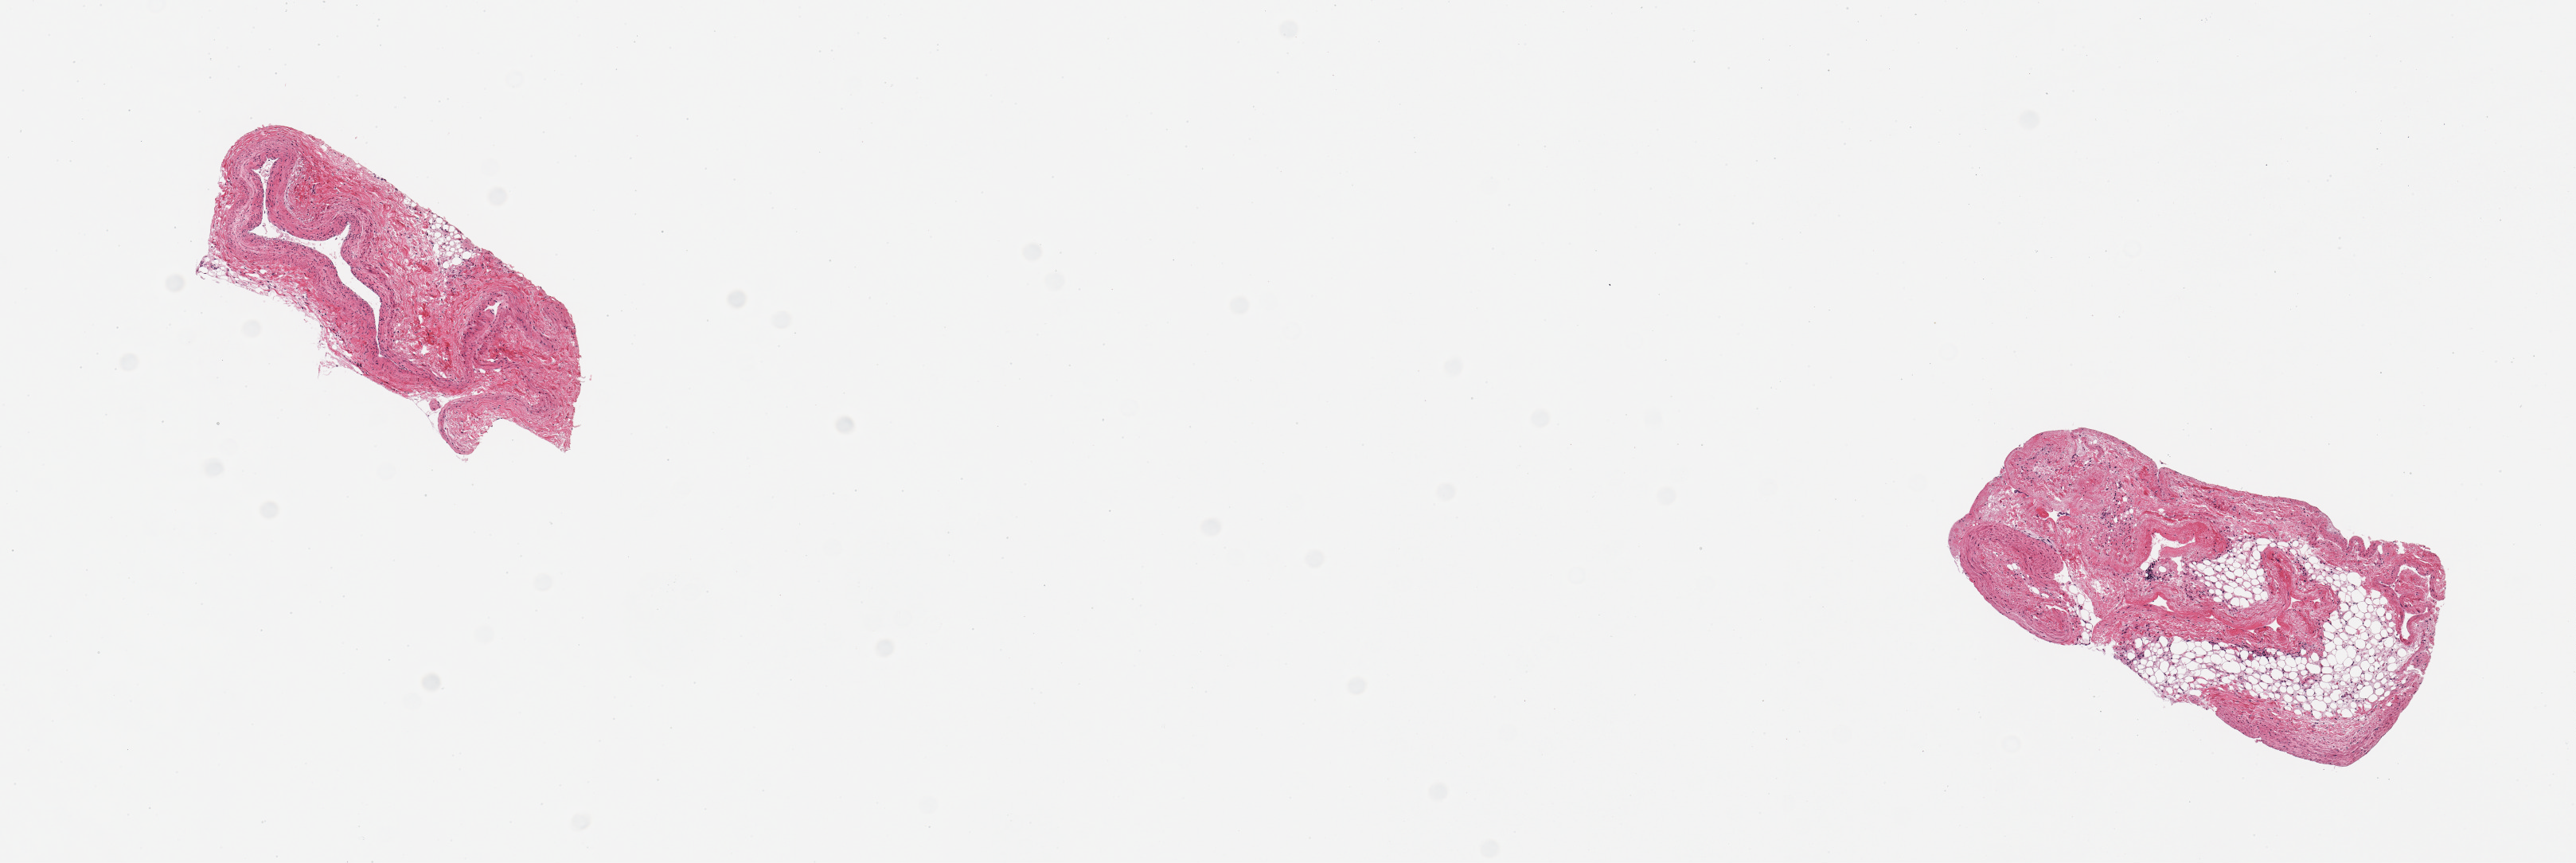
Digitized hematoxylin and eosin (H&E)-stained section, whole scanned area (about 12.8 x 4.3 mm) shown as a low-resolution overview; PAXgene-fixed paraffin-embedded (PFPE) section; section of coronary artery (target tissue); donor tissue sample. Male donor.
* pathologist's review note for this sample: 2 pieces; 50 & 20% fibroadipose content; venous elements admixed in 1 piece